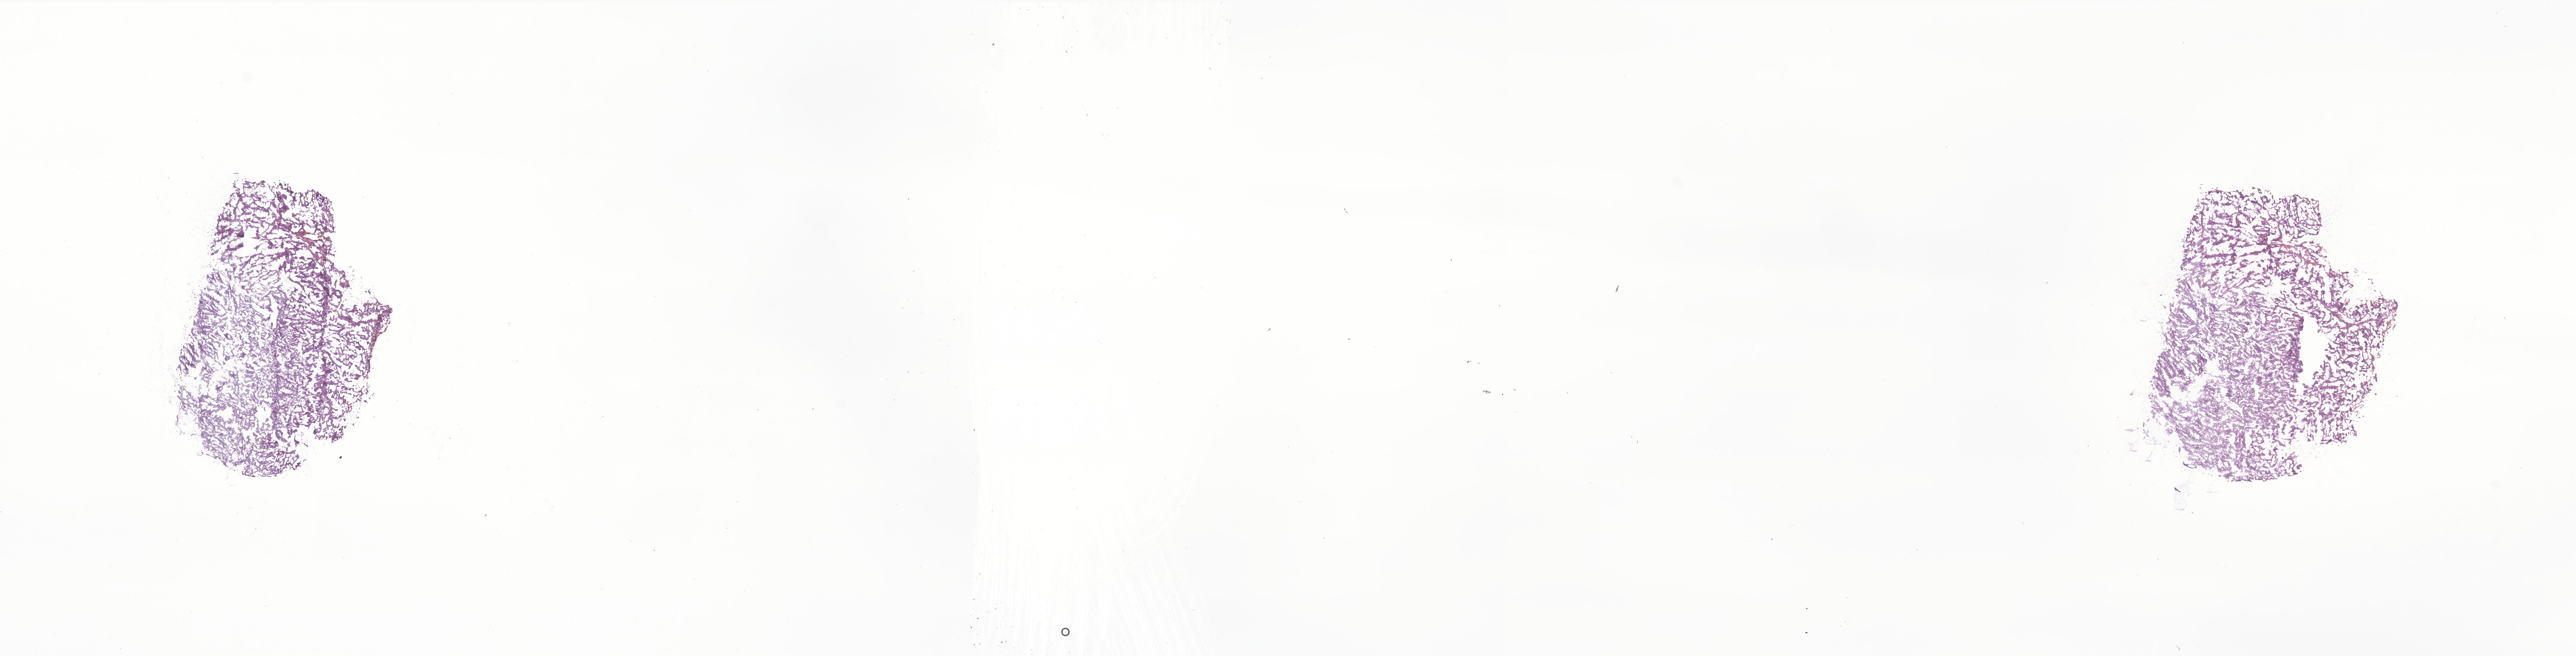
H&E whole-slide image of tumor tissue from the brain, a low-resolution overview of the entire scanned area, about 27.2 x 6.9 mm; frozen section. Patient male; age 65 days.
Recorded diagnosis: Atypical teratoid/rhabdoid tumor.